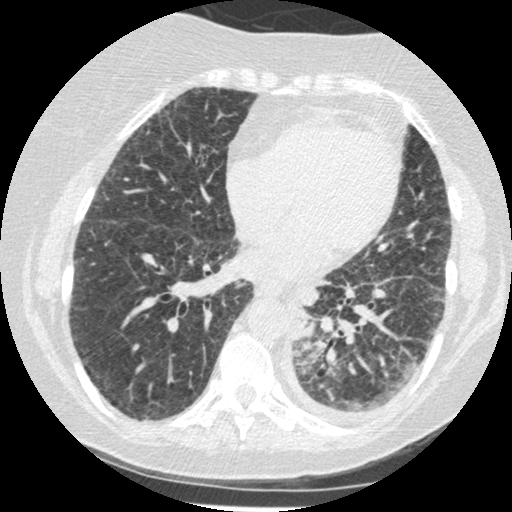
Chest CT (low-dose screening protocol), one axial image; third screening round (two years after baseline); lung window (W 1500 / L -600 HU); 1.25 mm slice thickness; slice 264 of 341 in the series. Female, age 60 years at enrolment. Former smoker at enrolment.
Expert-annotated lung lesion, bounding box <279,300,344,377> (left, top, right, bottom; pixels). Reader record for this screening exam (exam-level; its link to the box is not recorded): non-calcified nodule or mass ≥4 mm, left lower lobe, 54 × 38 mm, smooth margins, soft tissue attenuation, pre-existing on the prior screen: yes; interval growth: yes. Official screen result: positive, other. Later outcome: lung cancer diagnosed 15 days after this screen — small cell carcinoma, NOS, left lower lobe, undifferentiated (G4), stage IV (AJCC 6th edition), 69 mm at pathology.